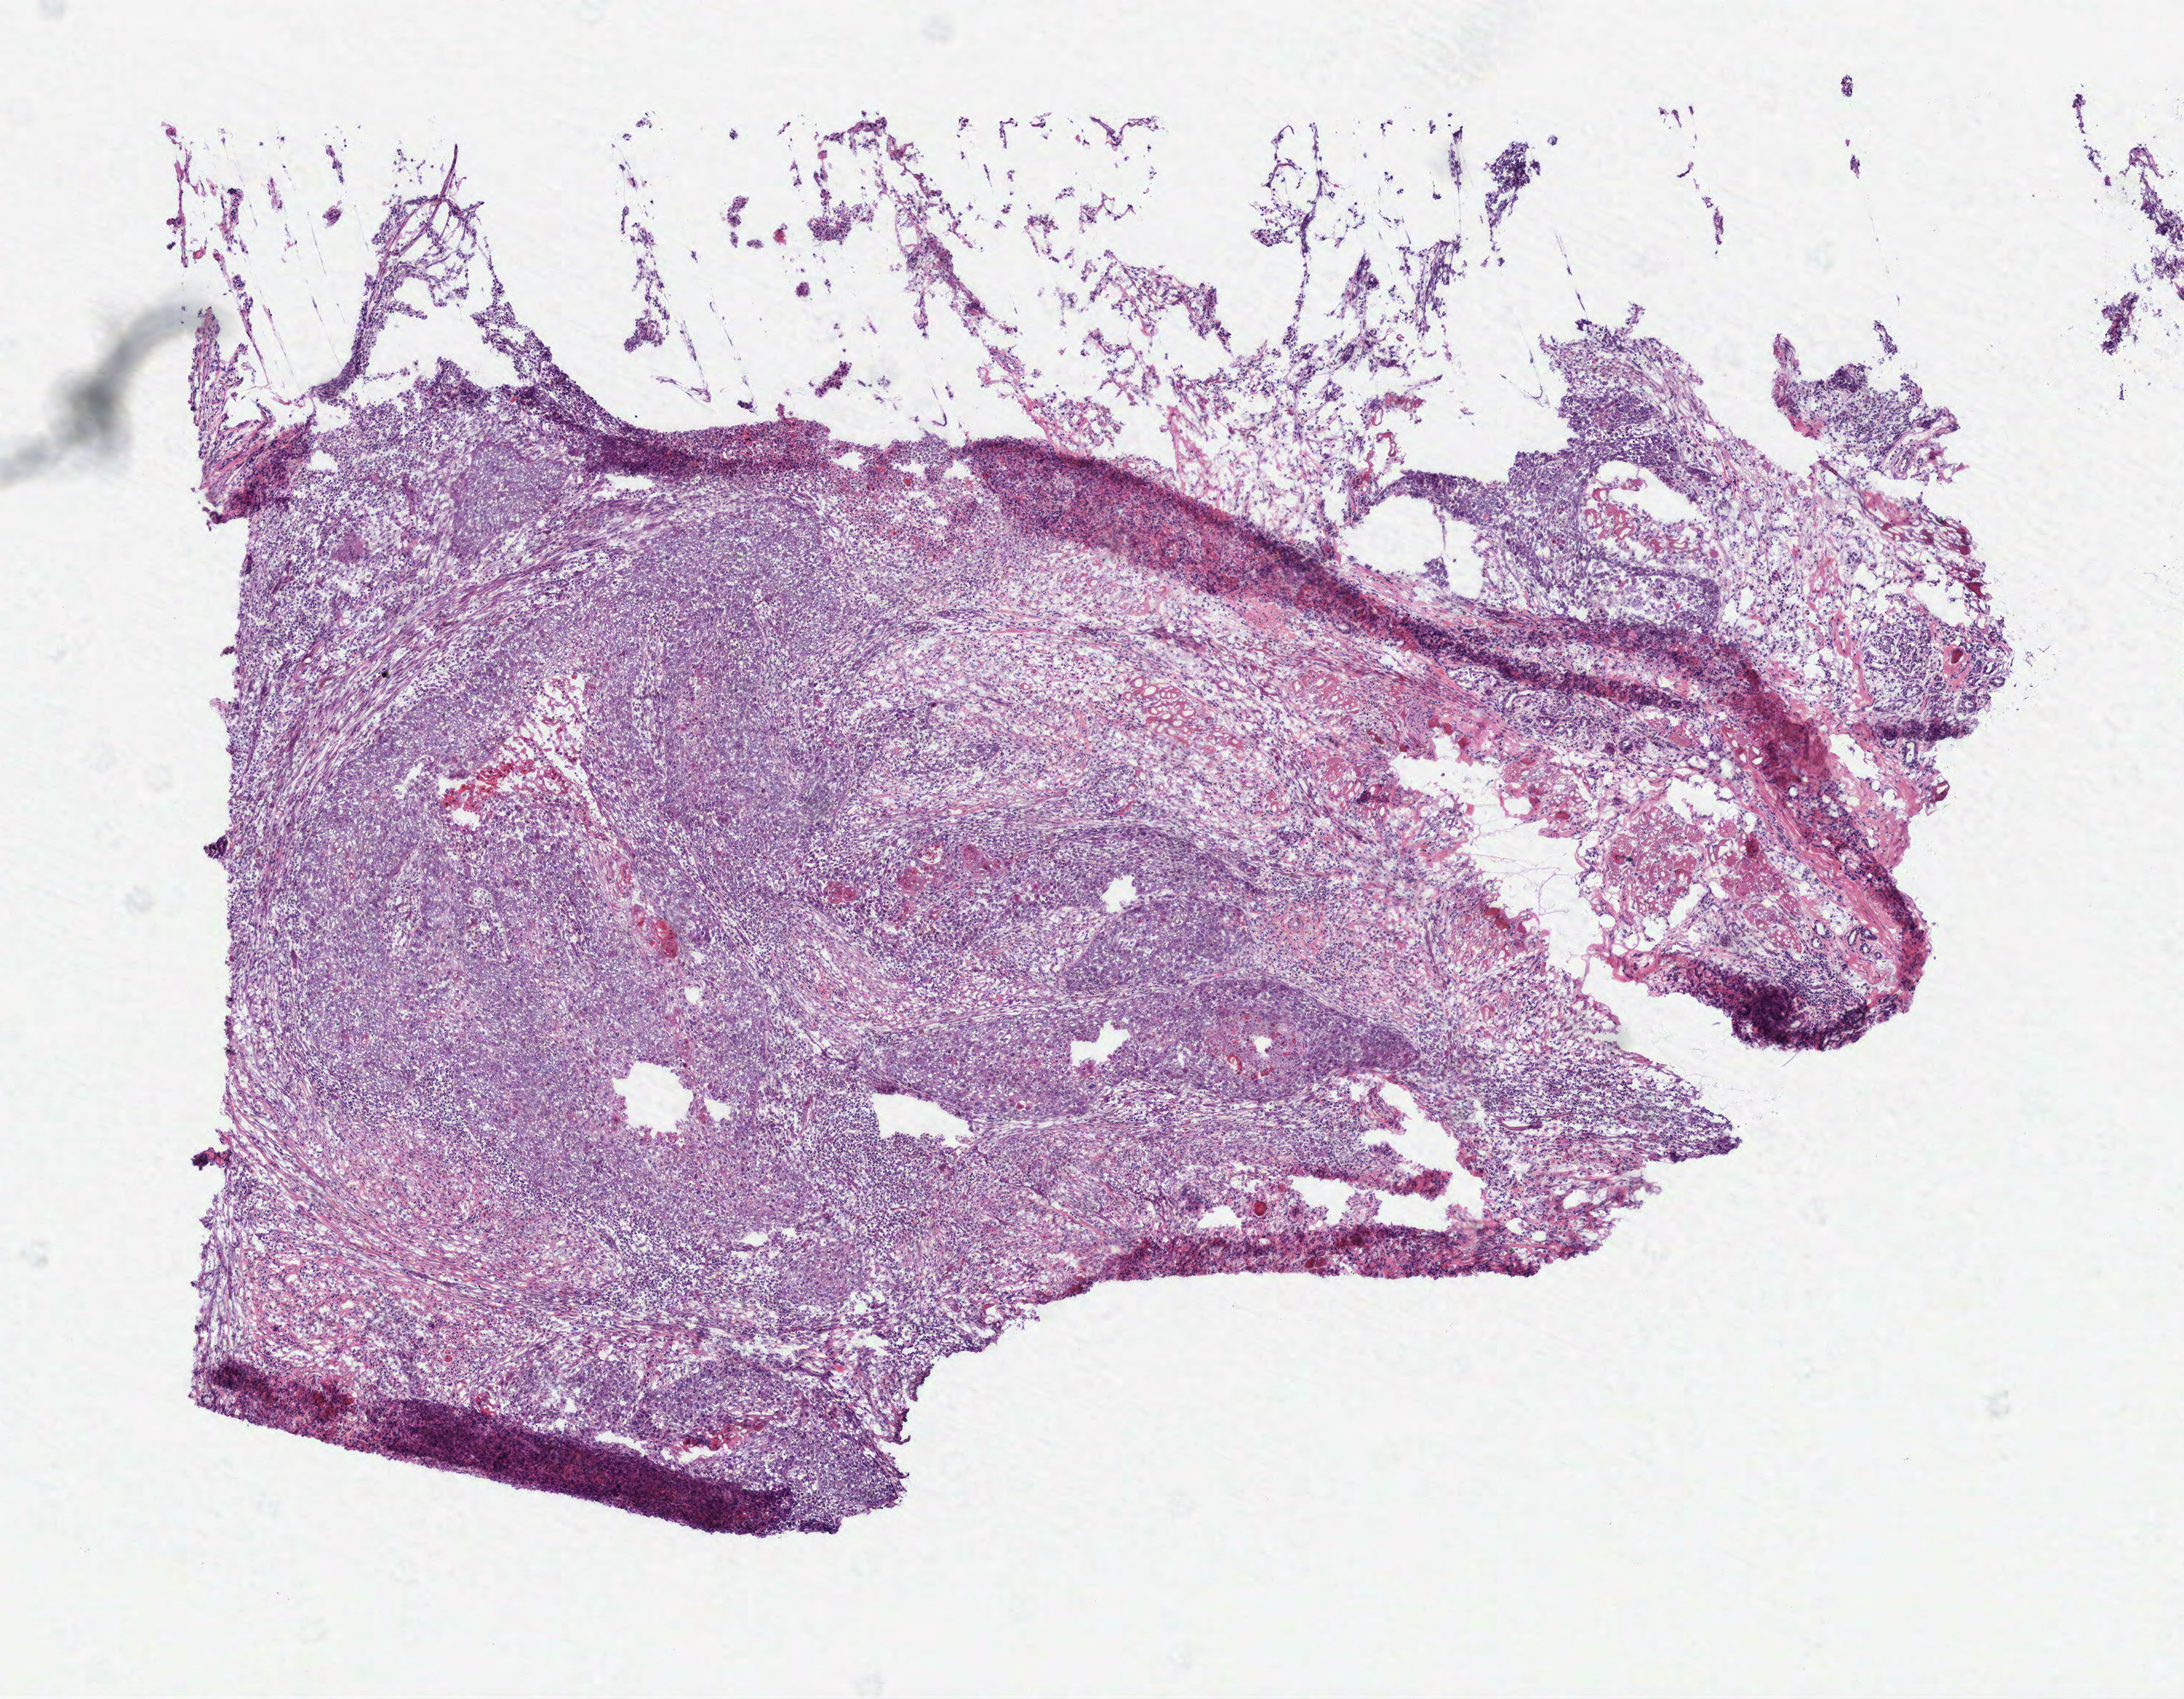
Whole-slide histology image, Hematoxylin and eosin (H&E) stained — low-resolution overview of the scanned area, about 6.0 x 4.7 mm (slide scanned at 40x), frozen section from the top of the tissue portion, sample: primary tumour, head and neck. Female, age 50 years at initial diagnosis. Histologic grade: G2 (moderately differentiated). Pathologist review of this section (percent, as recorded): tumour cells 82%, tumour nuclei 60%, normal cells 0%, stromal cells 15%, necrosis 3%.
TNM: T3 N2a. Laterality: right. Histologic diagnosis: Squamous cell carcinoma, NOS (tongue, NOS). AJCC pathologic stage: IVA.